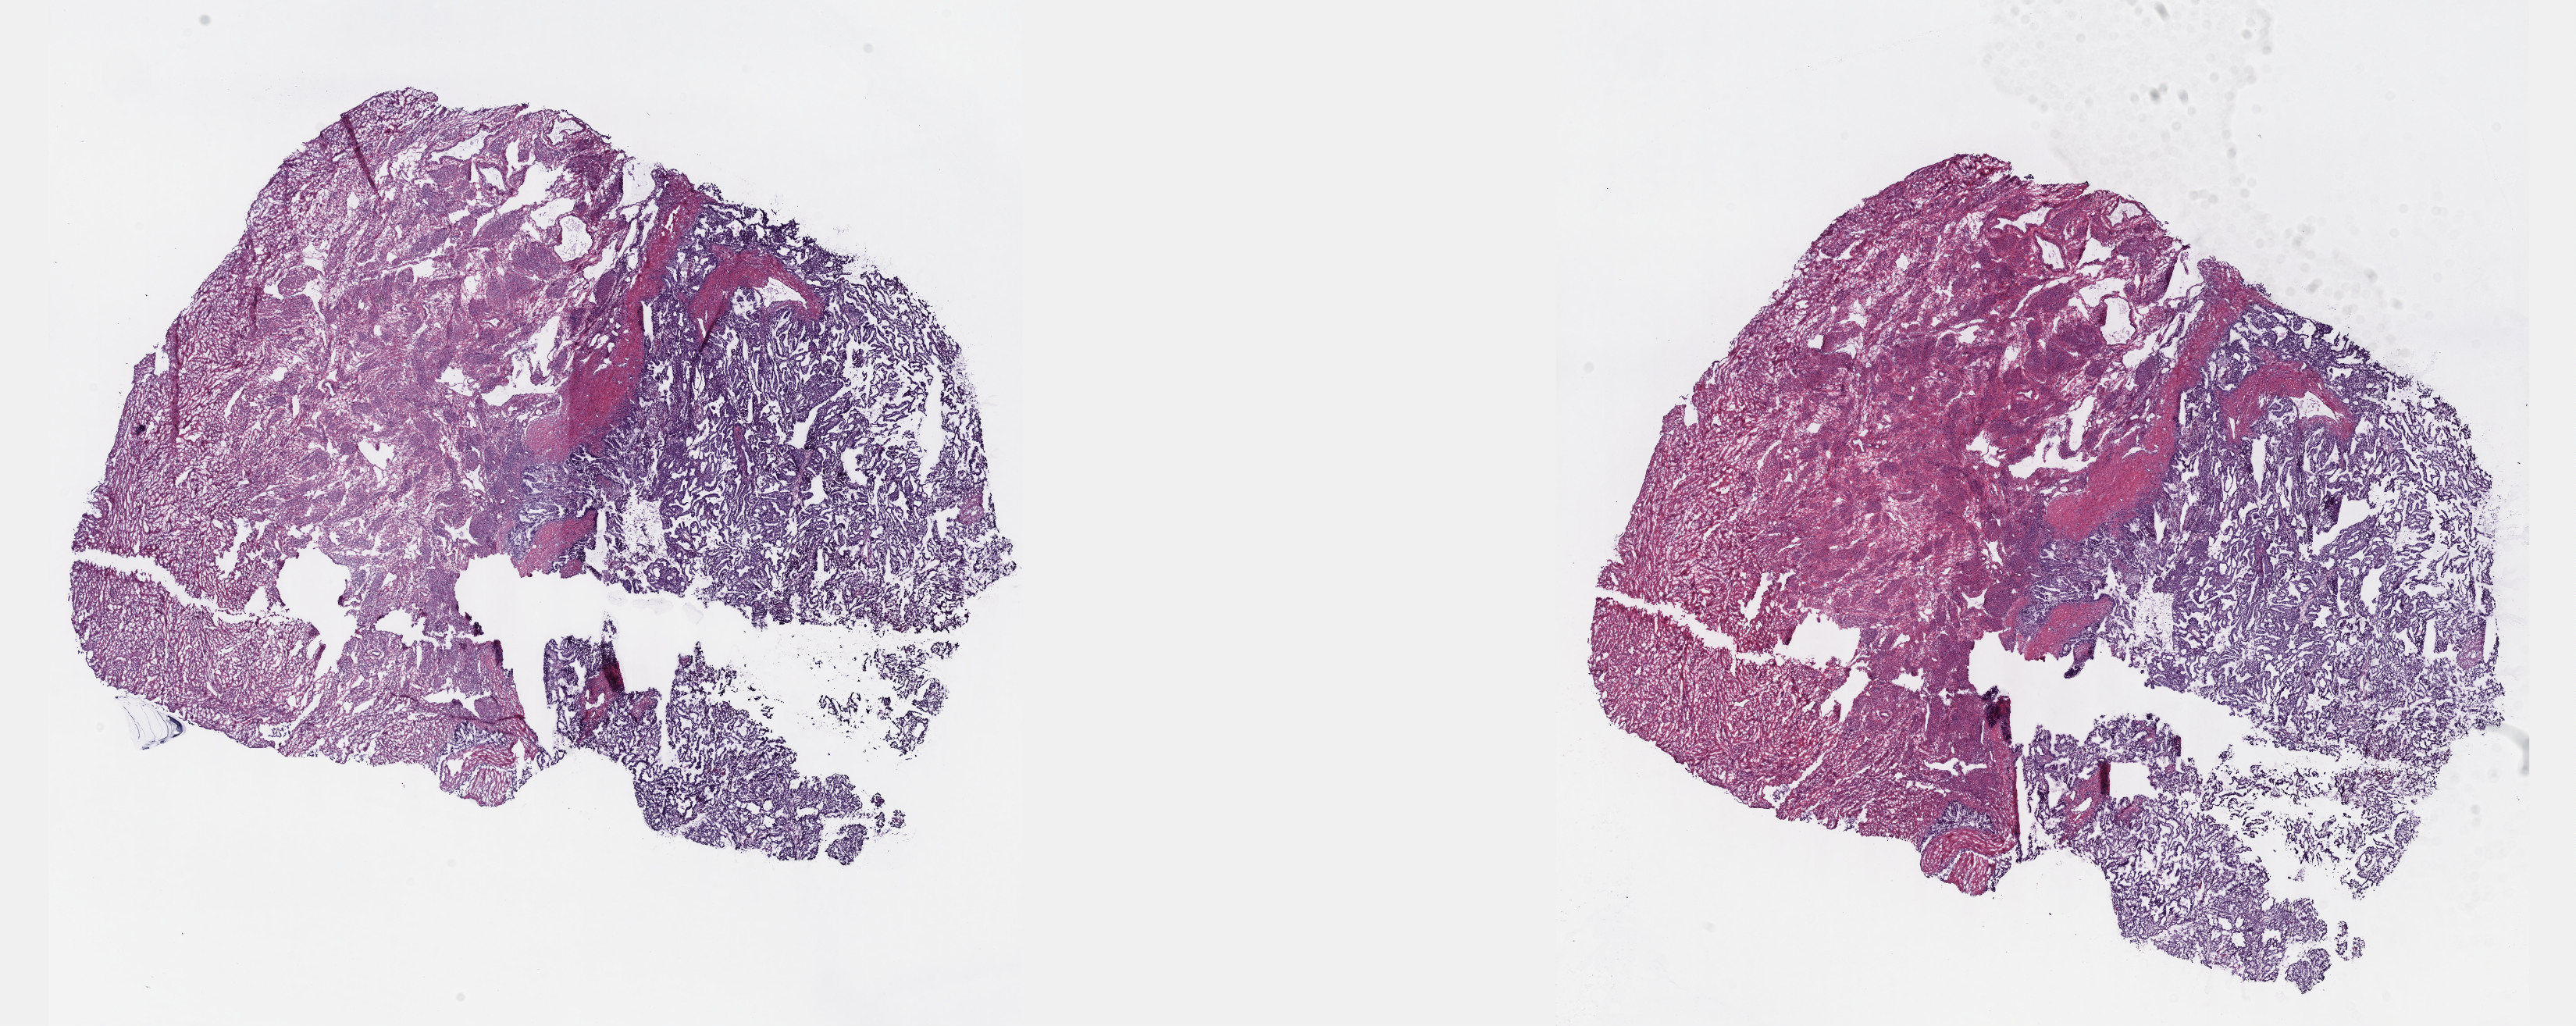
H&E-stained whole-slide image — a low-resolution overview of the entire scanned area, about 26.7 x 10.6 mm (slide scanned at 40x). Frozen section from the top of the tissue portion. Primary tumour sample from the uterus. Female patient; age at initial diagnosis 52 years. Histologic grade: G2 (moderately differentiated). Pathologist review of this section (percent, as recorded): tumour cells 60%, tumour nuclei 60%, normal cells 30%, stromal cells 10%, necrosis 0%. Inflammatory infiltration, as recorded: lymphocyte infiltration 5%, monocyte infiltration 0%, neutrophil infiltration 0%.
FIGO stage: II. Lymph nodes positive (case pathology): 0 of 6 examined. Diagnosis: Endometrioid adenocarcinoma, NOS.